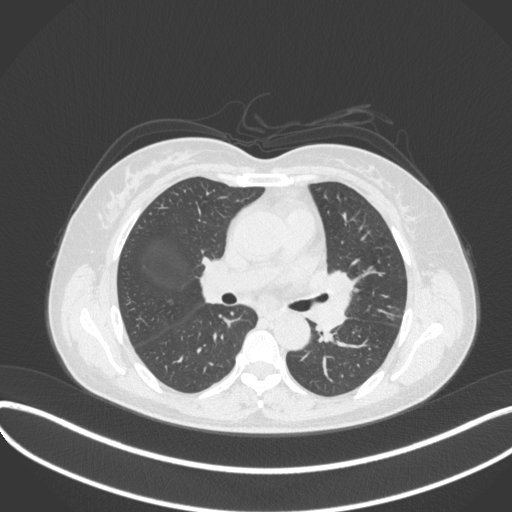
Chest CT, one axial slice. Position 199 of 373 along the scan axis. Reconstruction kernel B31f. 120 kVp. Lung window (W 1500 / L -600 HU). 1 mm slice thickness. 512 × 512 image matrix, field of view 400 × 400 mm. Patient: female, 54 years. From the clinical record (not read from this slice): clinical TNM (as recorded): T2a N1 M0.
Structures marked on this image (rectangle marked by the reading radiologist):
- lung tumour (recorded histology: small cell carcinoma): bounding box [x1, y1, x2, y2] px = [313, 266, 357, 337]